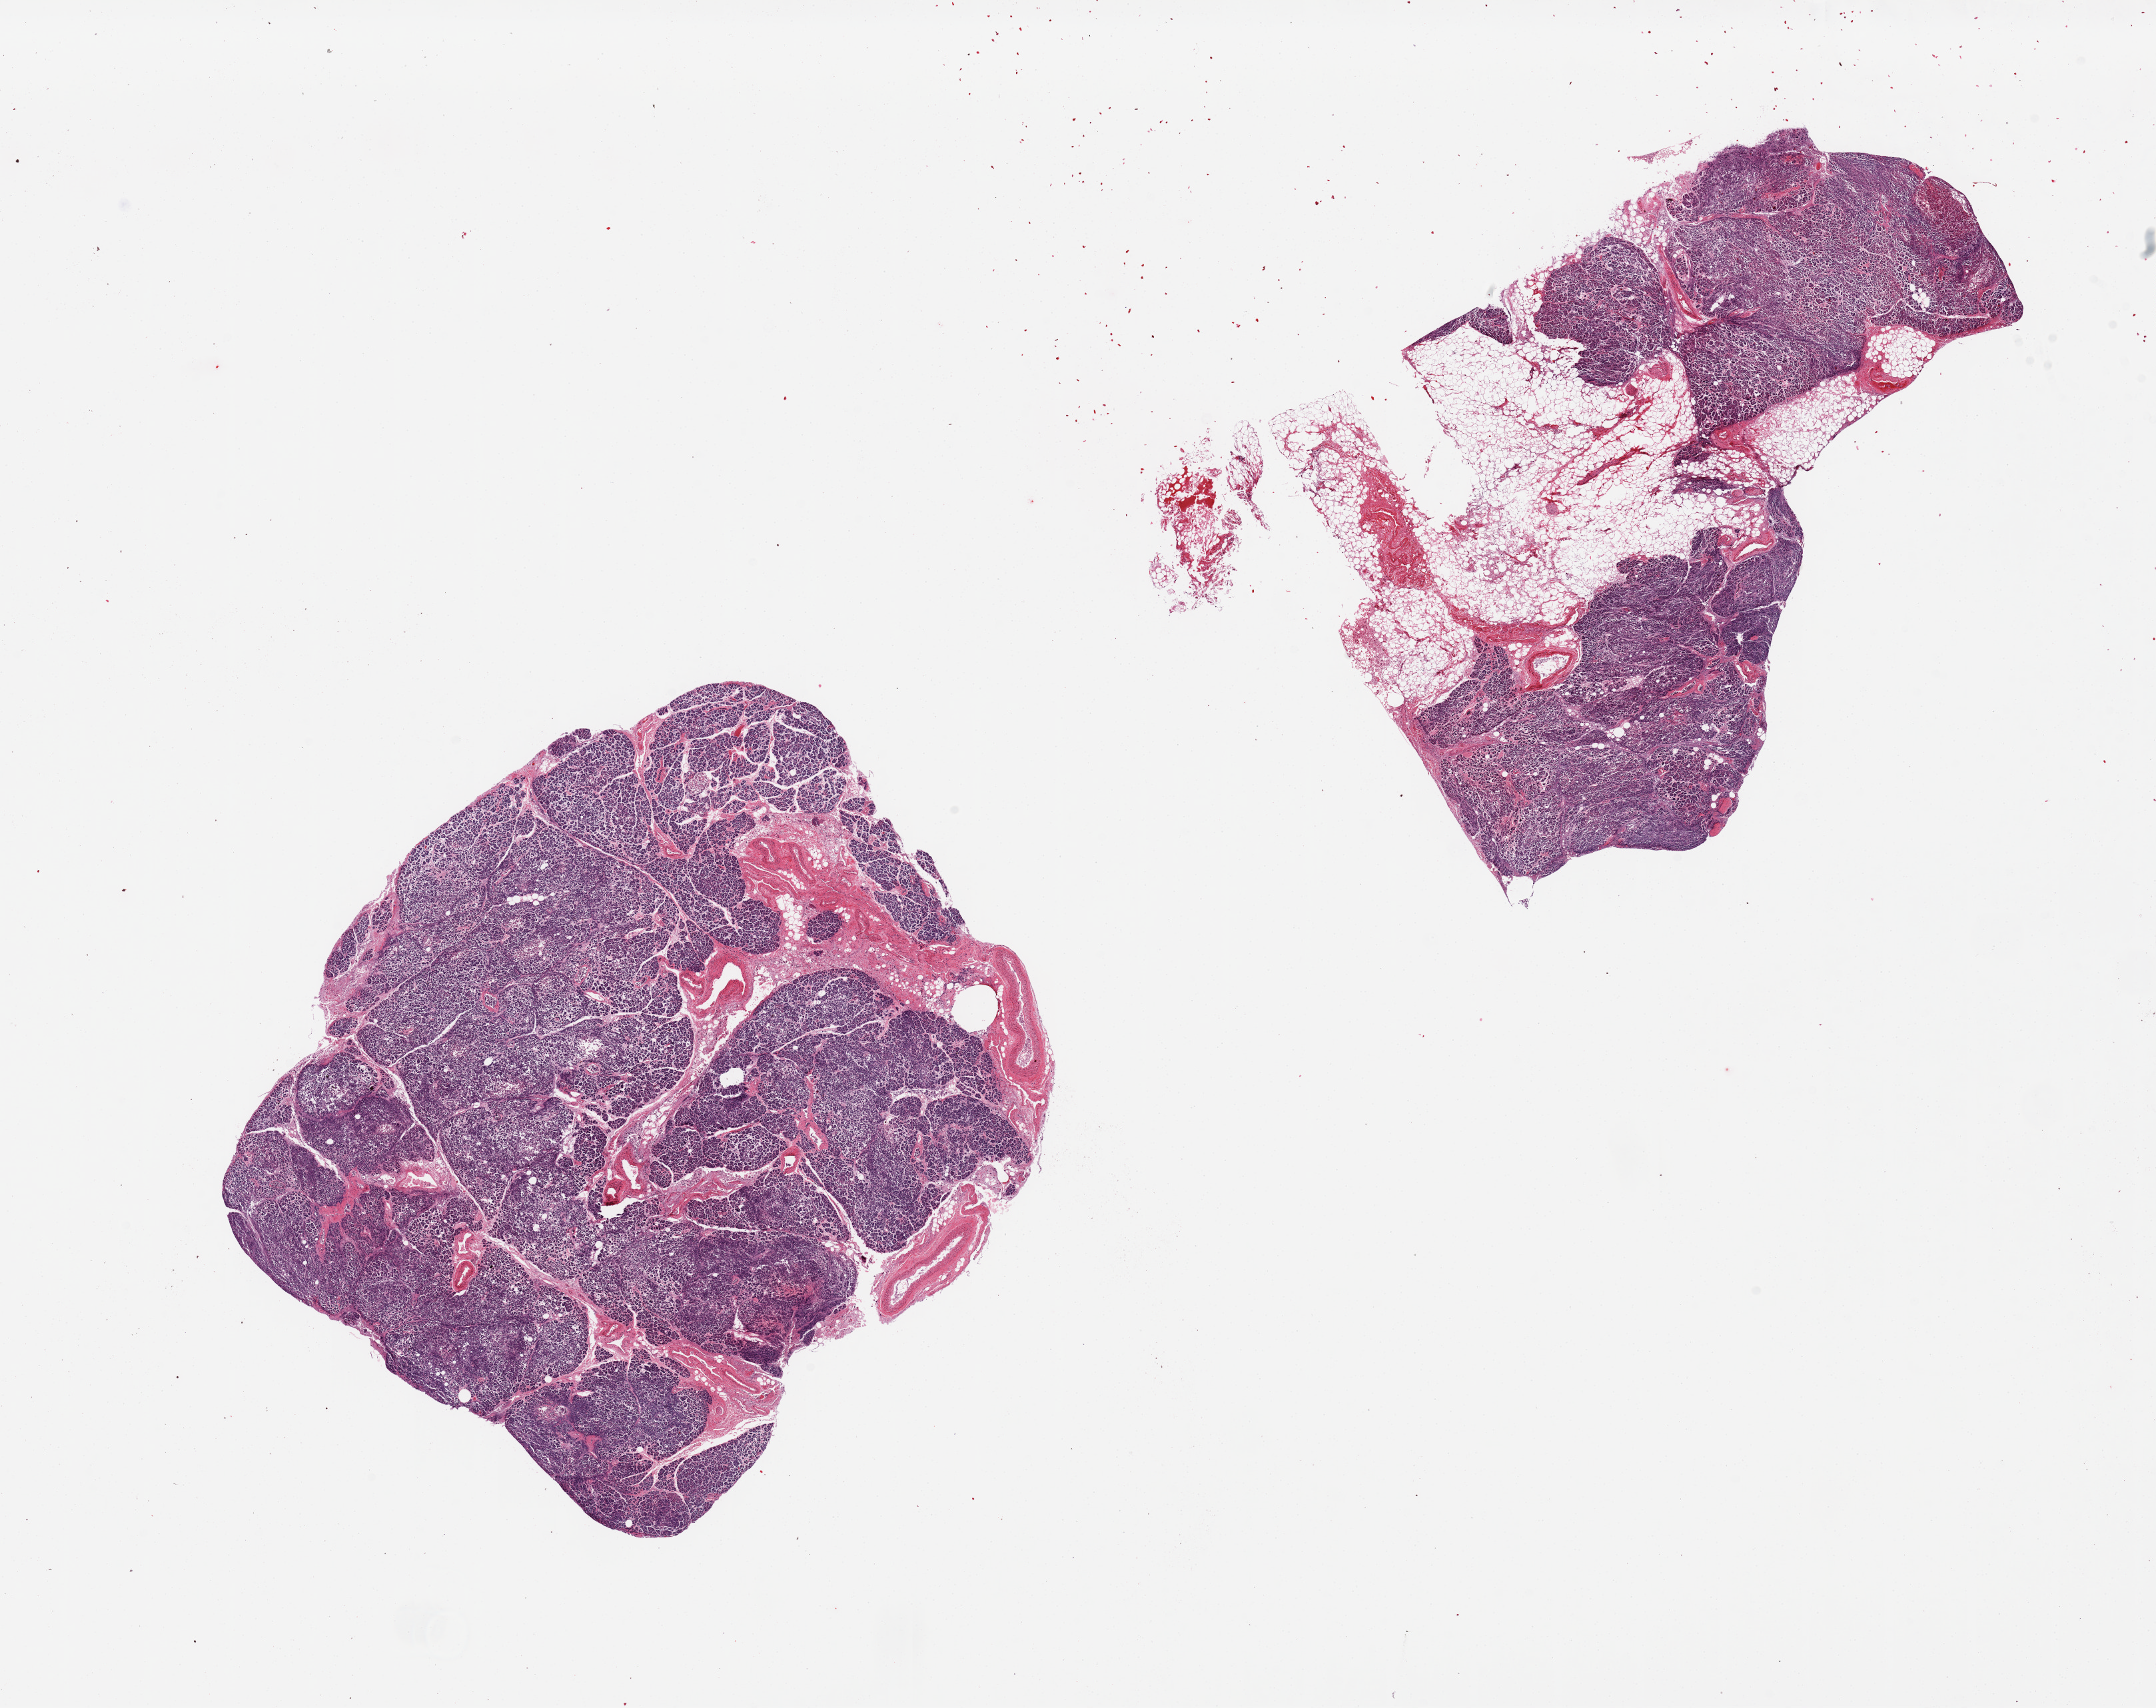
Digitized hematoxylin and eosin (H&E)-stained section, brightfield — low-resolution overview of the scanned area, about 25.6 x 20.3 mm. PAXgene-fixed, paraffin-embedded tissue. Target tissue: pancreas. Tissue donor sample. Donor: male.
Pathologist's review note for this sample: 2 pieces, 1 piece is ~40% fat.